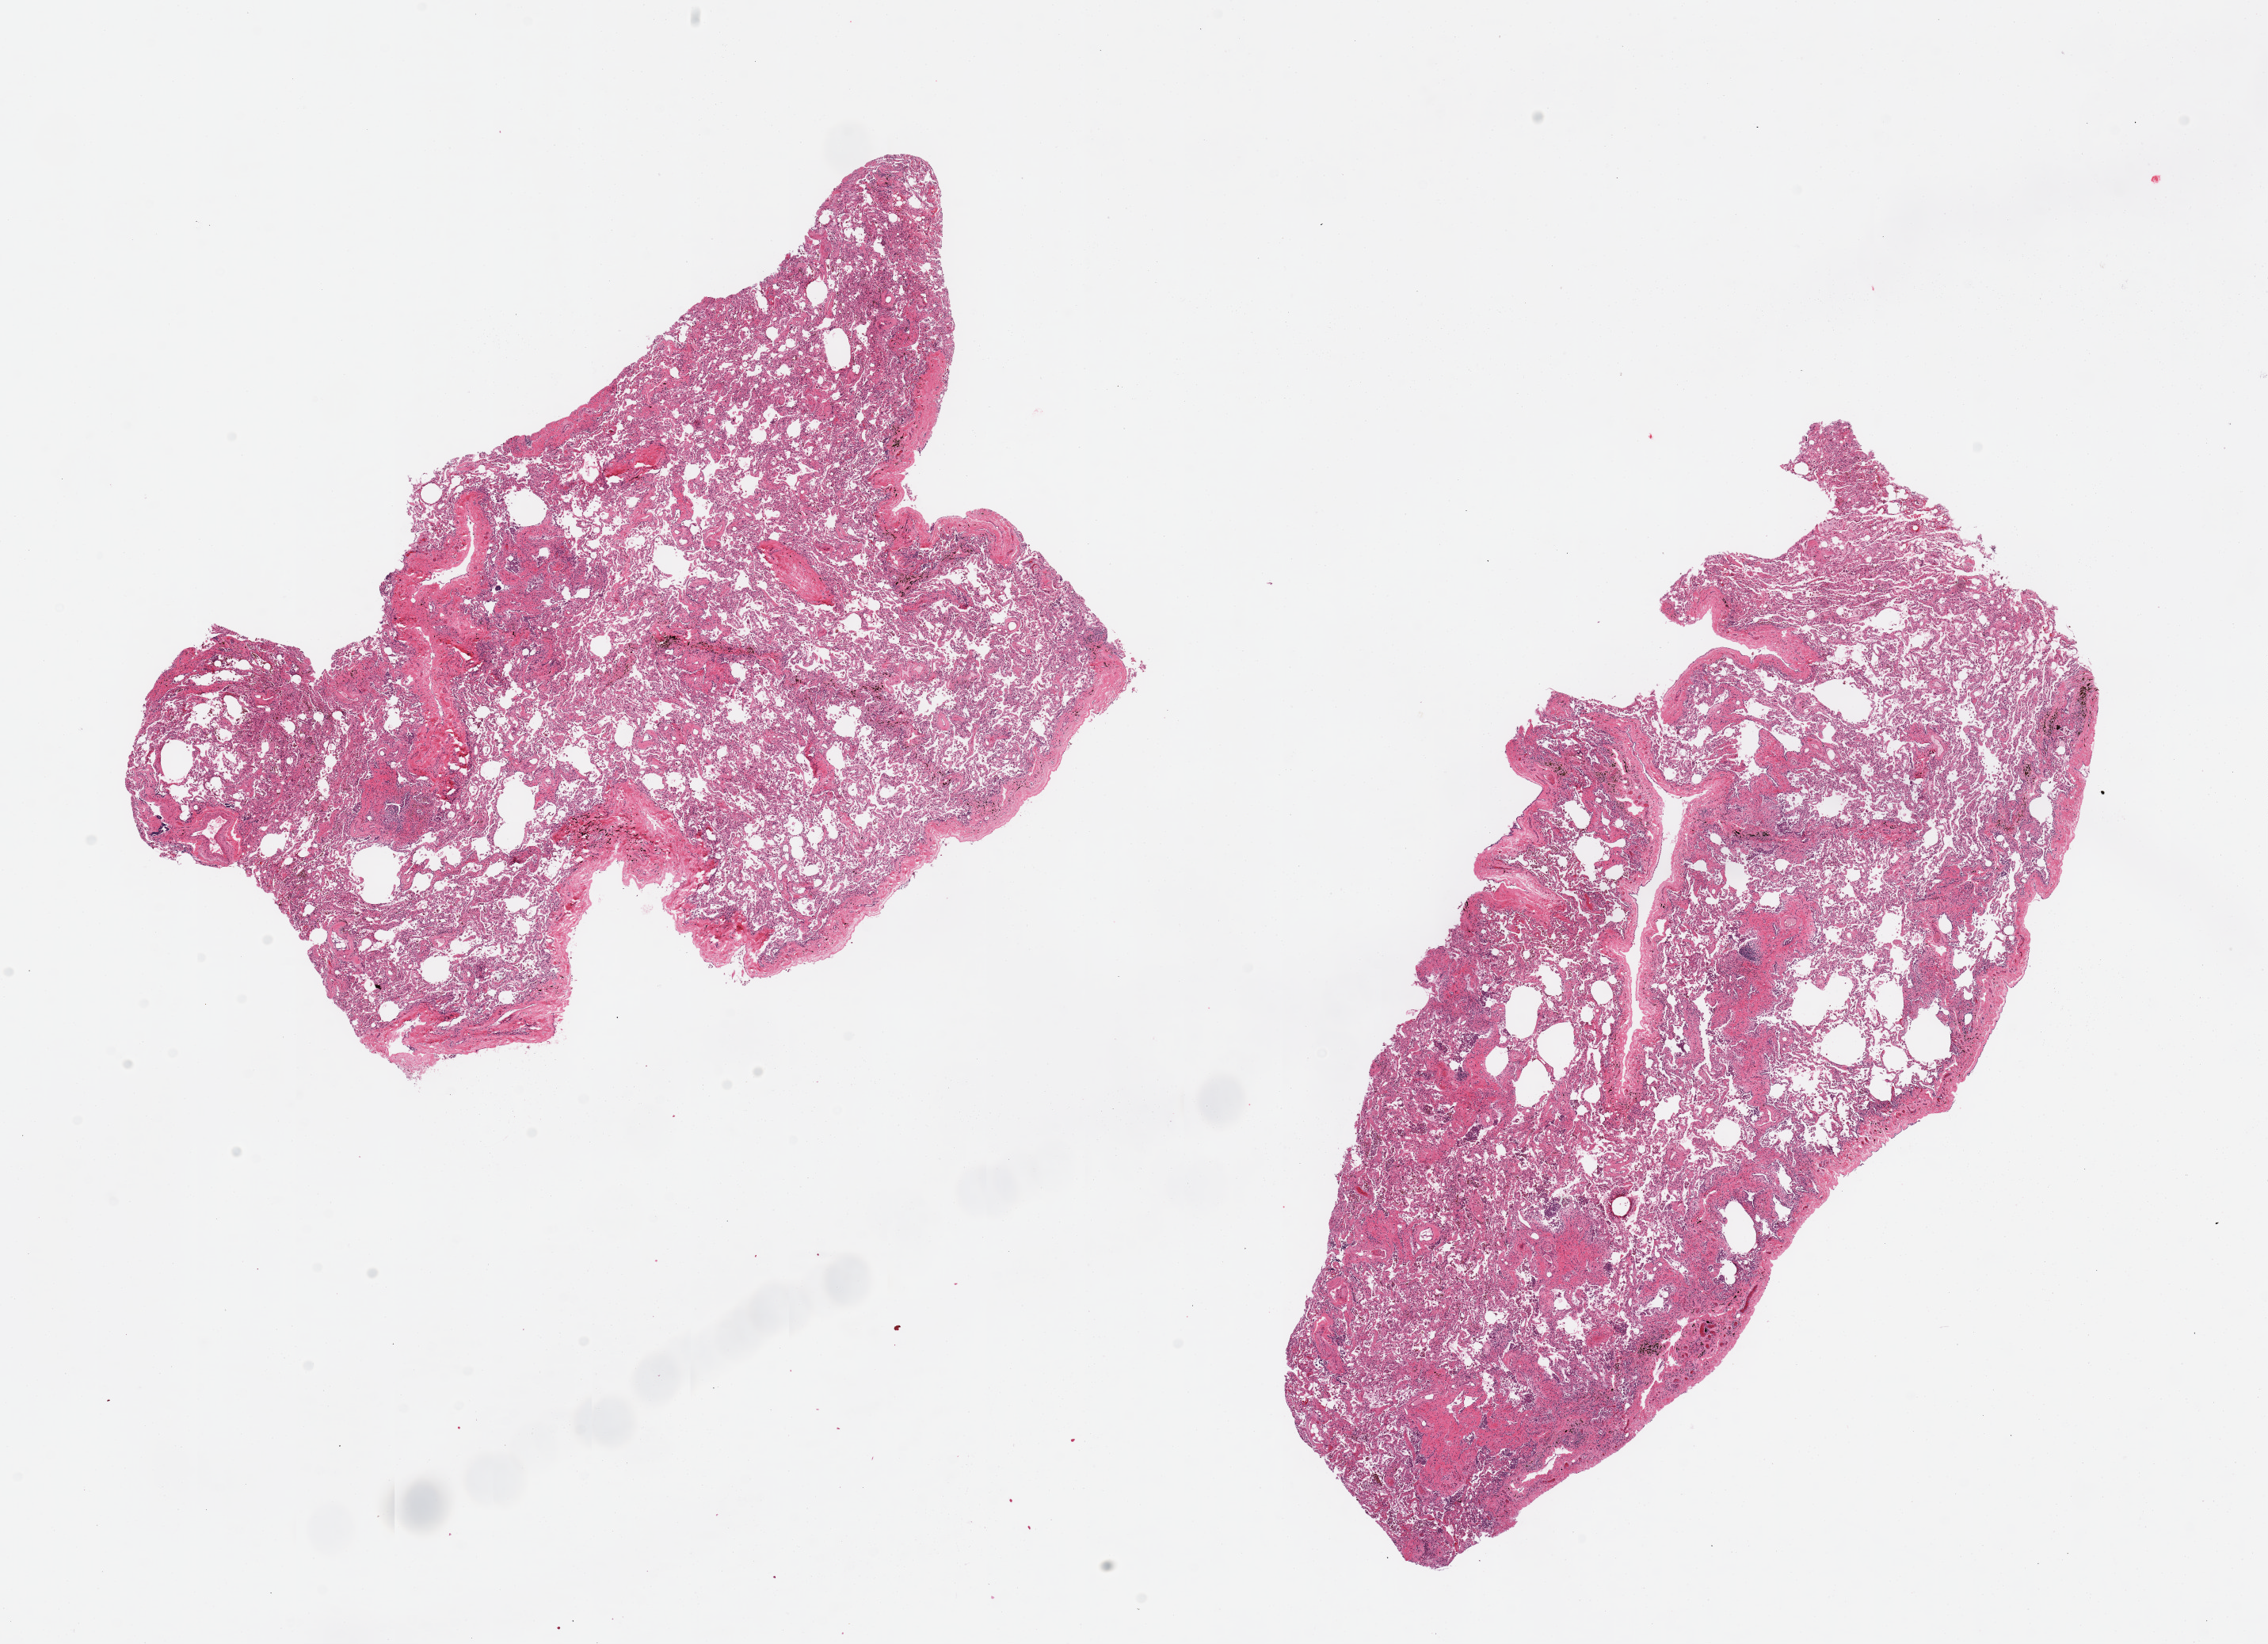
Whole-slide image, hematoxylin and eosin (H&E) stain, whole scanned area (about 22.6 x 16.4 mm) shown as a low-resolution overview, PAXgene-fixed paraffin-embedded (PFPE) section, sampled site (target tissue): lung, tissue donor sample.
- pathologist's review note for this sample: 2 pieces; pleura included; thick walled vessels; thick alveolar walls; hemosiderin laden histiocytes